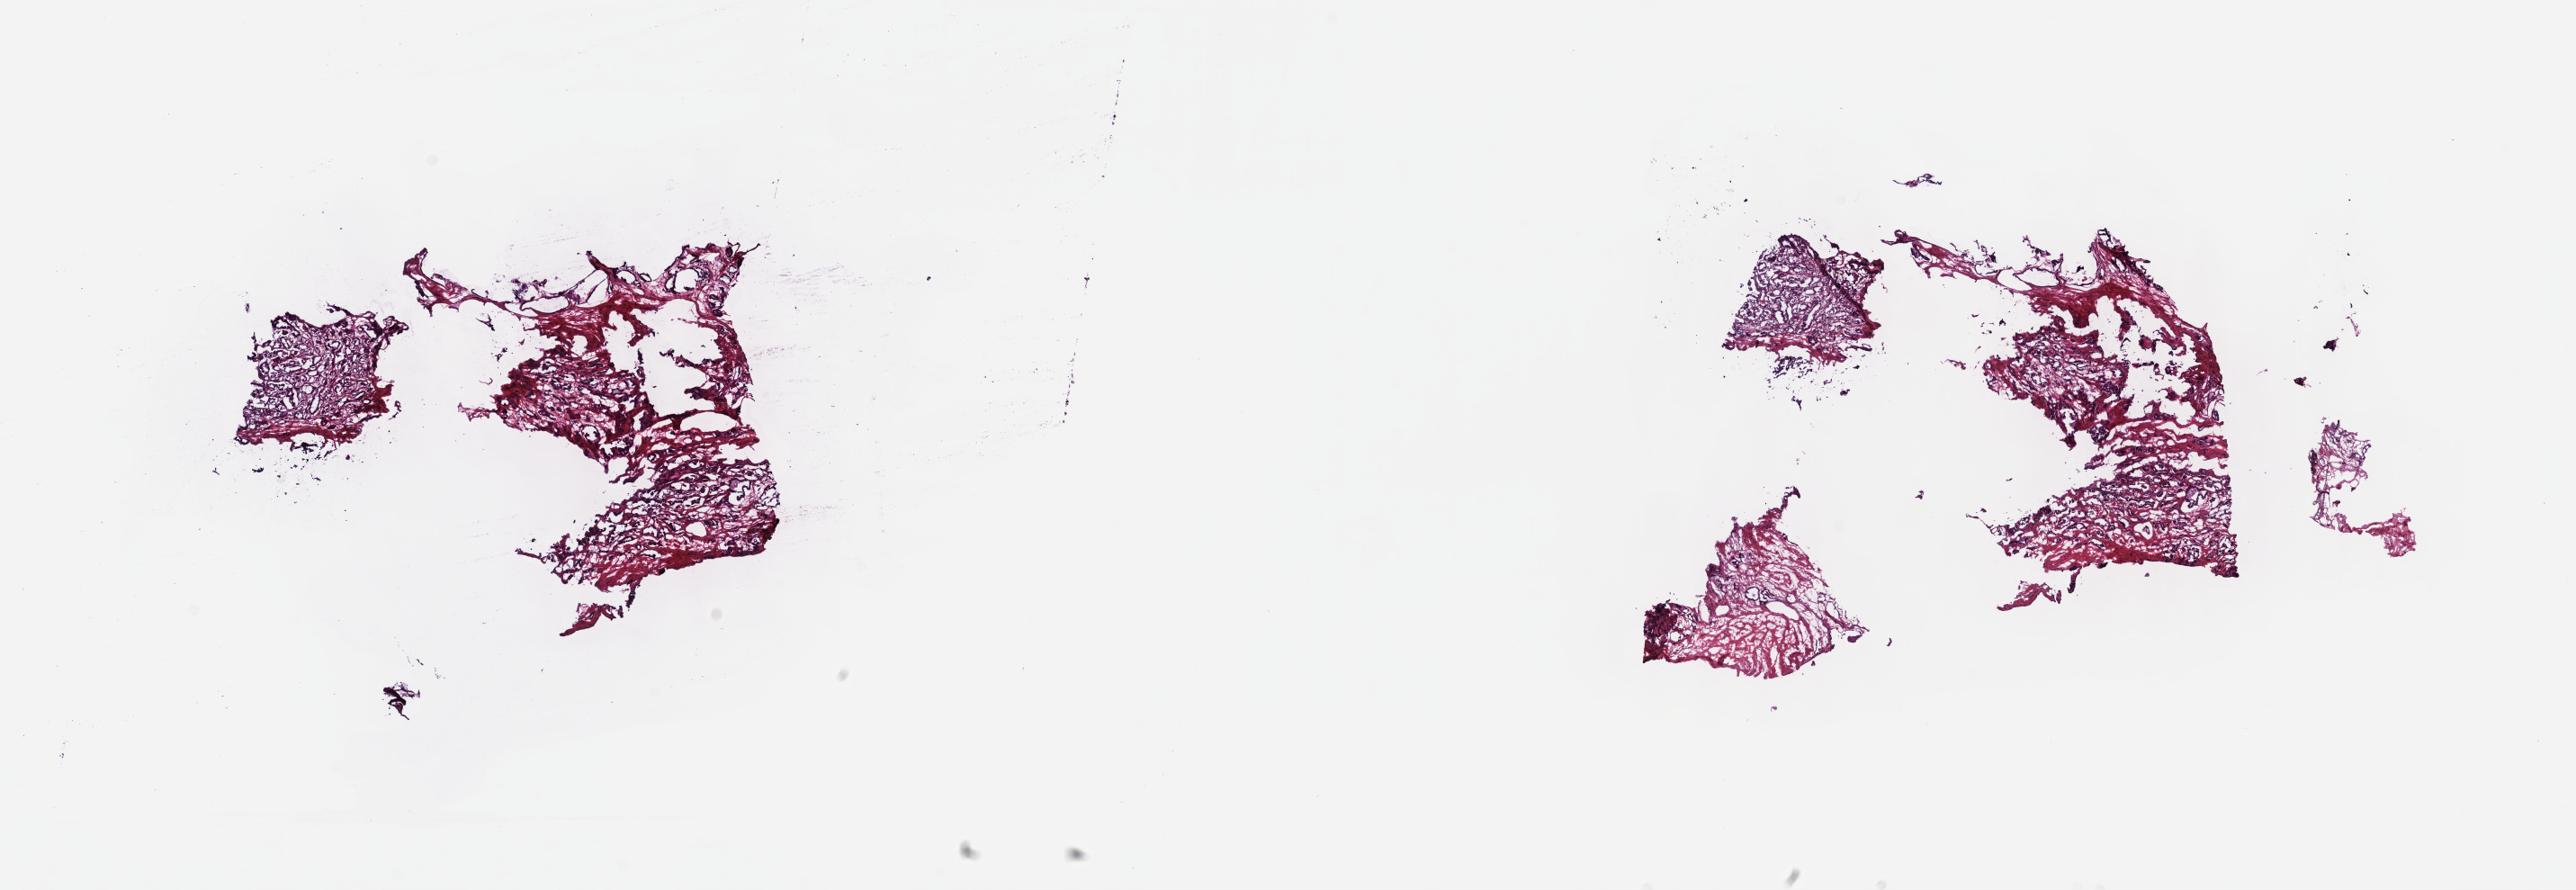
H&E whole-slide image — whole scanned area (about 23.2 x 8.0 mm) shown as a low-resolution overview. Frozen section from the top of the tissue portion. Prostate, primary tumour sample. Male patient; age at initial diagnosis 68 years. Gleason score: 7 (4+3). Slide review estimates, as recorded: tumour cells 50%, tumour nuclei 60%, normal cells 50%, stromal cells 0%, necrosis 0%. Infiltration values recorded for this section: lymphocyte infiltration 0%, monocyte infiltration 0%, neutrophil infiltration 0%.
Lymph nodes positive (case pathology): 0 of 7 examined. Laterality: bilateral. Diagnosis: Adenocarcinoma, NOS (prostate gland).